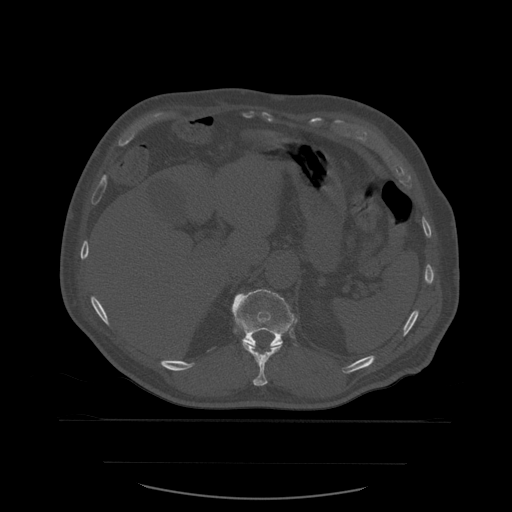
CT including the spine, one axial slice. Position 284 of 590 along the scan axis. Bone window (W 1800 / L 400 HU). 1.25 mm slice thickness. 512 × 512 image matrix, field of view 479 × 479 mm. Patient age 71 years. Case-level facts recorded for this patient, not image findings: primary cancer: lung; vertebrae with lytic lesions (as recorded): T1, T2, L5, S1.
Annotated regions visible in this slice (semi-automatically segmented with operator editing):
- T11 vertebra: bounding box <242,343,282,386> (left, top, right, bottom; pixels)
- T12 vertebra: <232,289,298,348>